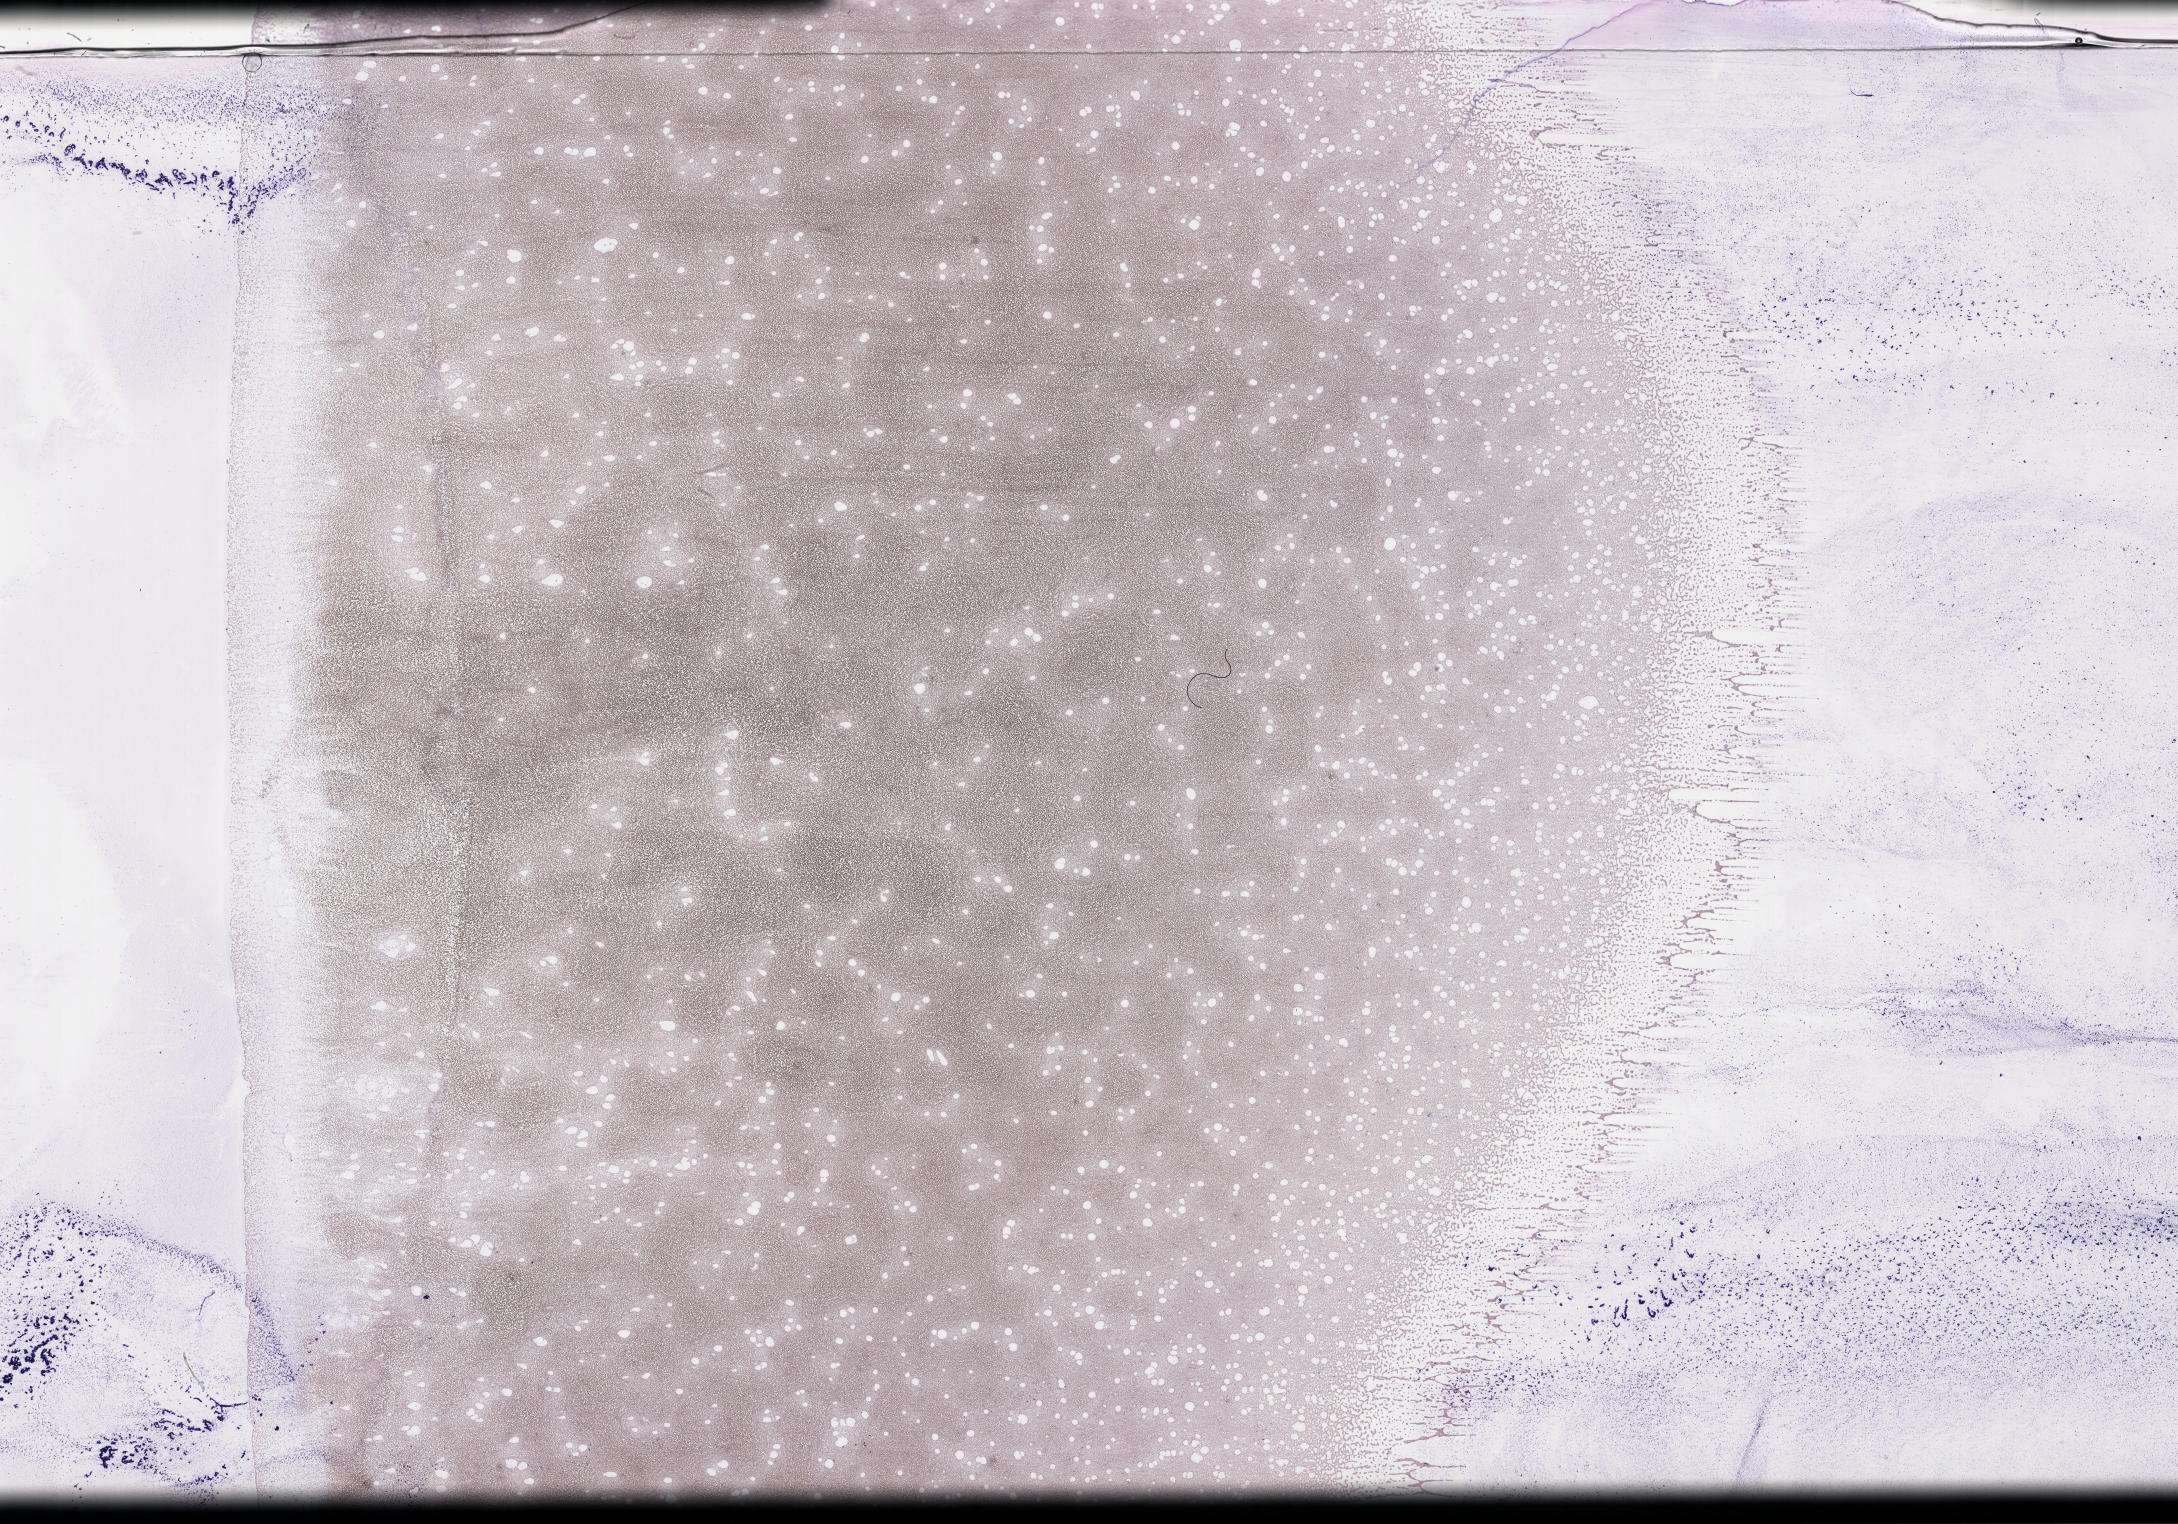
Wright-Giemsa-stained whole blood smear, whole-slide image — shown as a low-resolution overview of the whole scanned area (about 35.2 x 24.6 mm); EDTA-anticoagulated smear; specimen time point: collected on treatment. Patient sex: male.
From a patient with: Plasma Cell Myeloma.